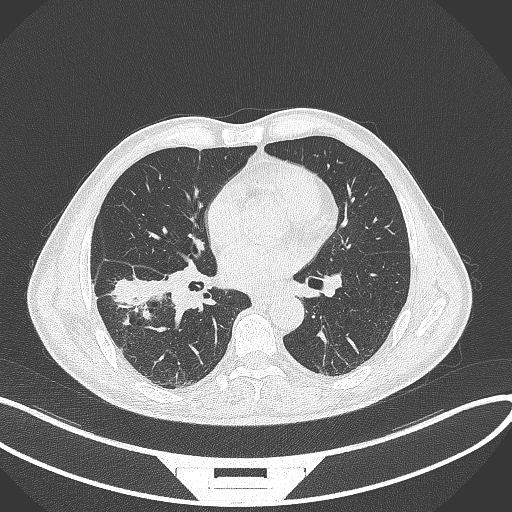
Chest CT, one axial slice; slice 170 of 364 in the series (ordered by position); reconstruction kernel B70f; 120 kVp; lung window (W 1500 / L -600 HU); 1 mm slice thickness; 512 × 512 image matrix. Male patient, age 58 years. From the clinical record (not read from this slice): clinical TNM (as recorded): T3 N0 M0; histopathological grade: G2.
Structures marked on this image (bounding box drawn by a radiologist):
- lung tumour (recorded histology: squamous cell carcinoma): bounding box <115,275,175,308> (left, top, right, bottom; pixels)